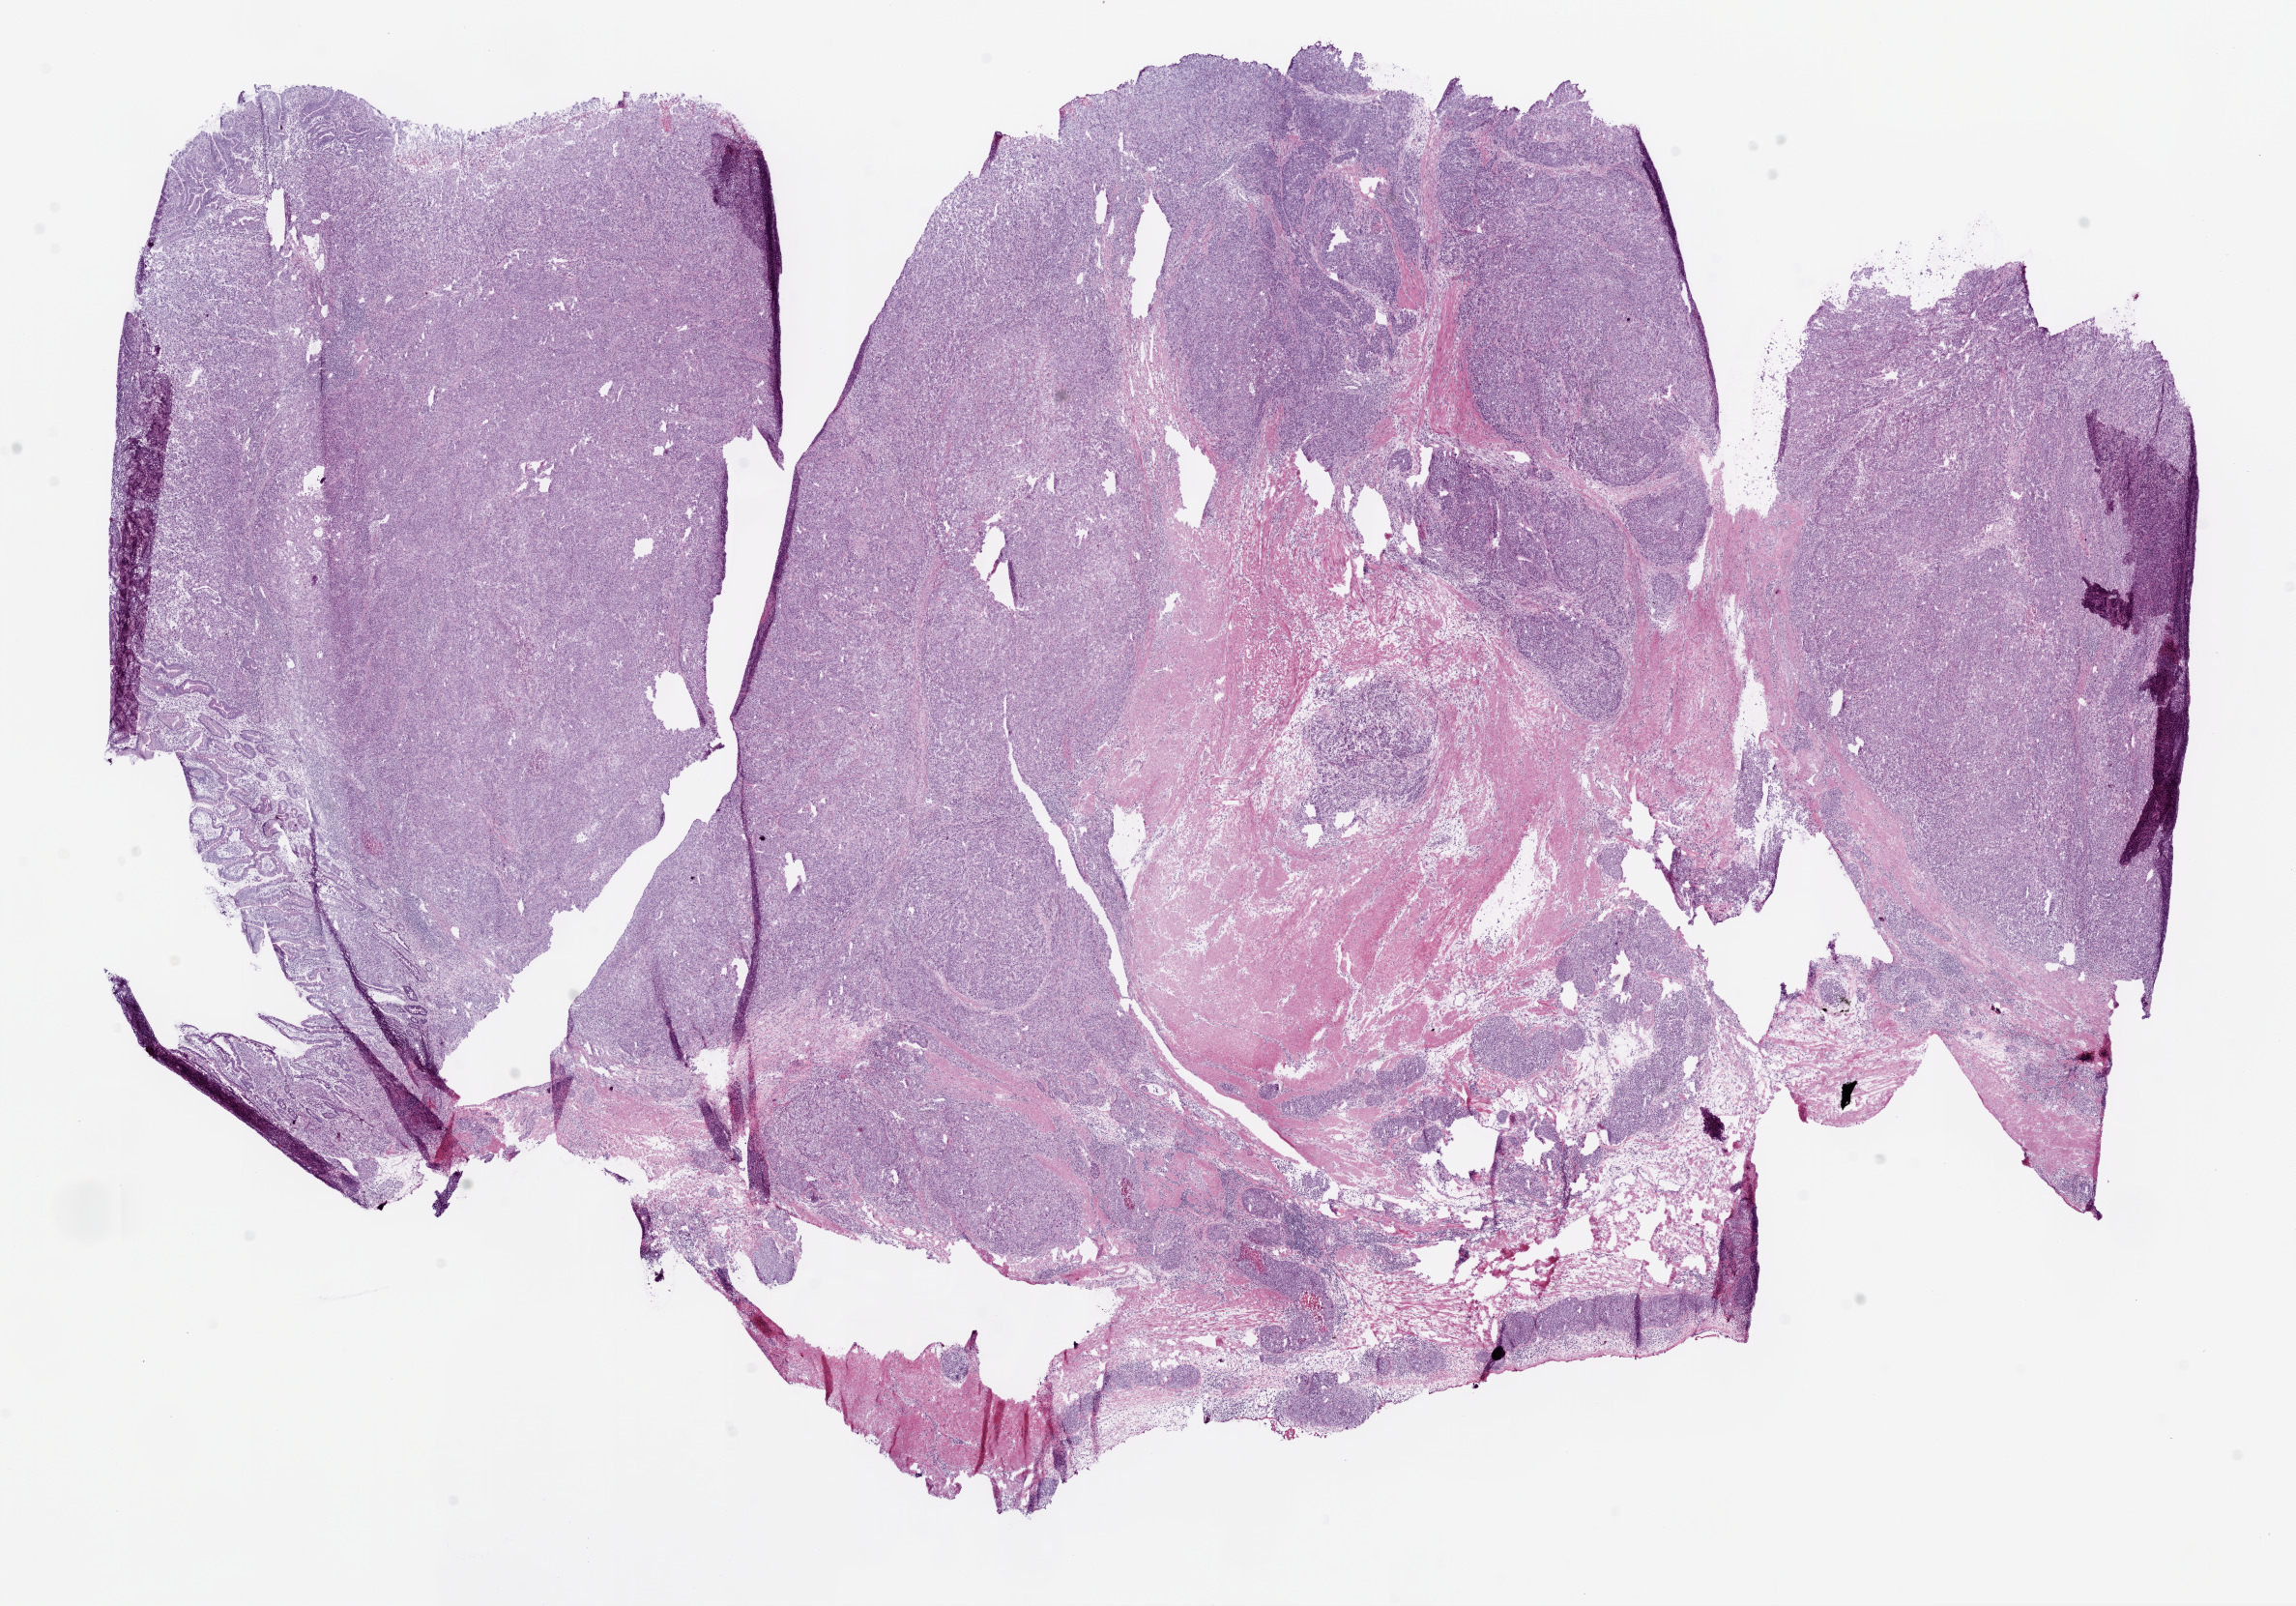
Hematoxylin and eosin (H&E) stained whole-slide image — low-resolution overview of the scanned area, about 19.1 x 13.3 mm (slide scanned at 20x); frozen section from the top of the tissue portion; stomach, primary tumour sample. Female patient; age at initial diagnosis 78 years. Histologic grade: G3 (poorly differentiated). Slide review estimates, as recorded: tumour cells 75%, tumour nuclei 70%, normal cells 5%, stromal cells 15%, necrosis 5%.
• histologic diagnosis: Adenocarcinoma, NOS (gastric antrum)
• AJCC pathologic stage: IV